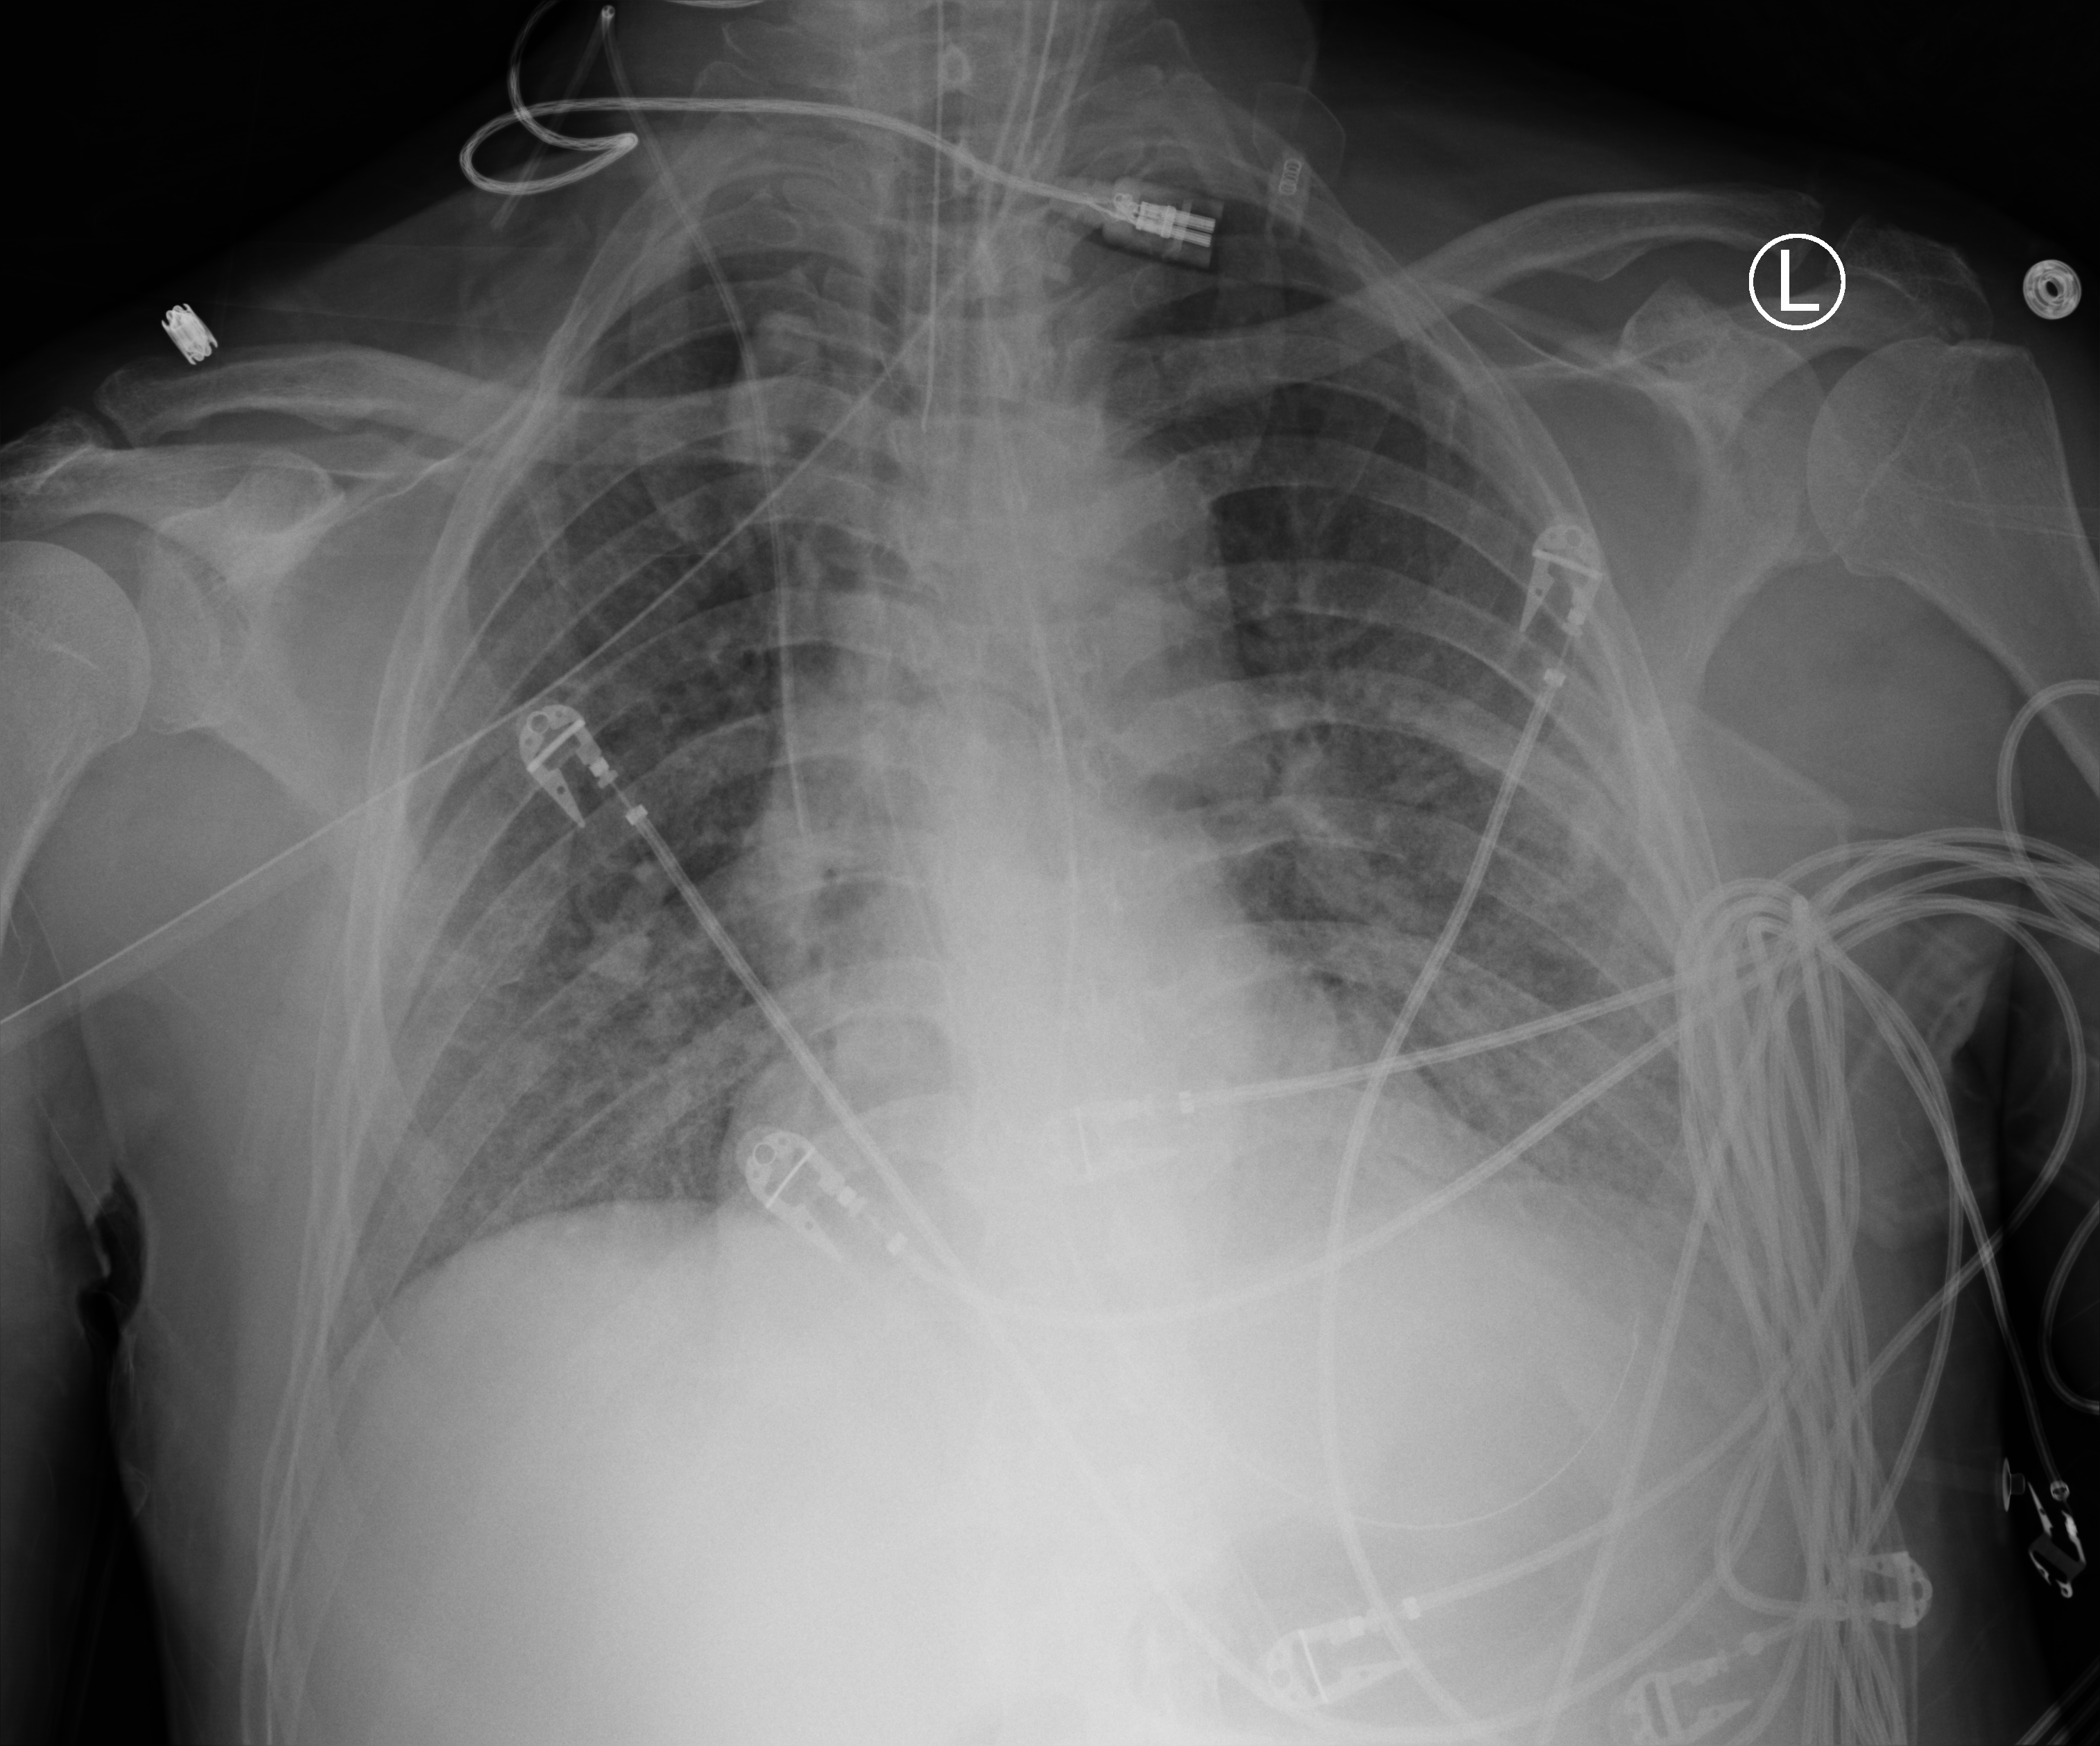
Bedside chest radiograph (computed radiography), anteroposterior (AP) projection. Patient hospitalised with COVID-19; male, aged 60–74 years.
Hospital-stay facts (about this admission, not read from this image; timing relative to this image not recorded): length of hospital stay: 37 days; other chronic lung disease (admission record): no; hypertension (admission record): yes.